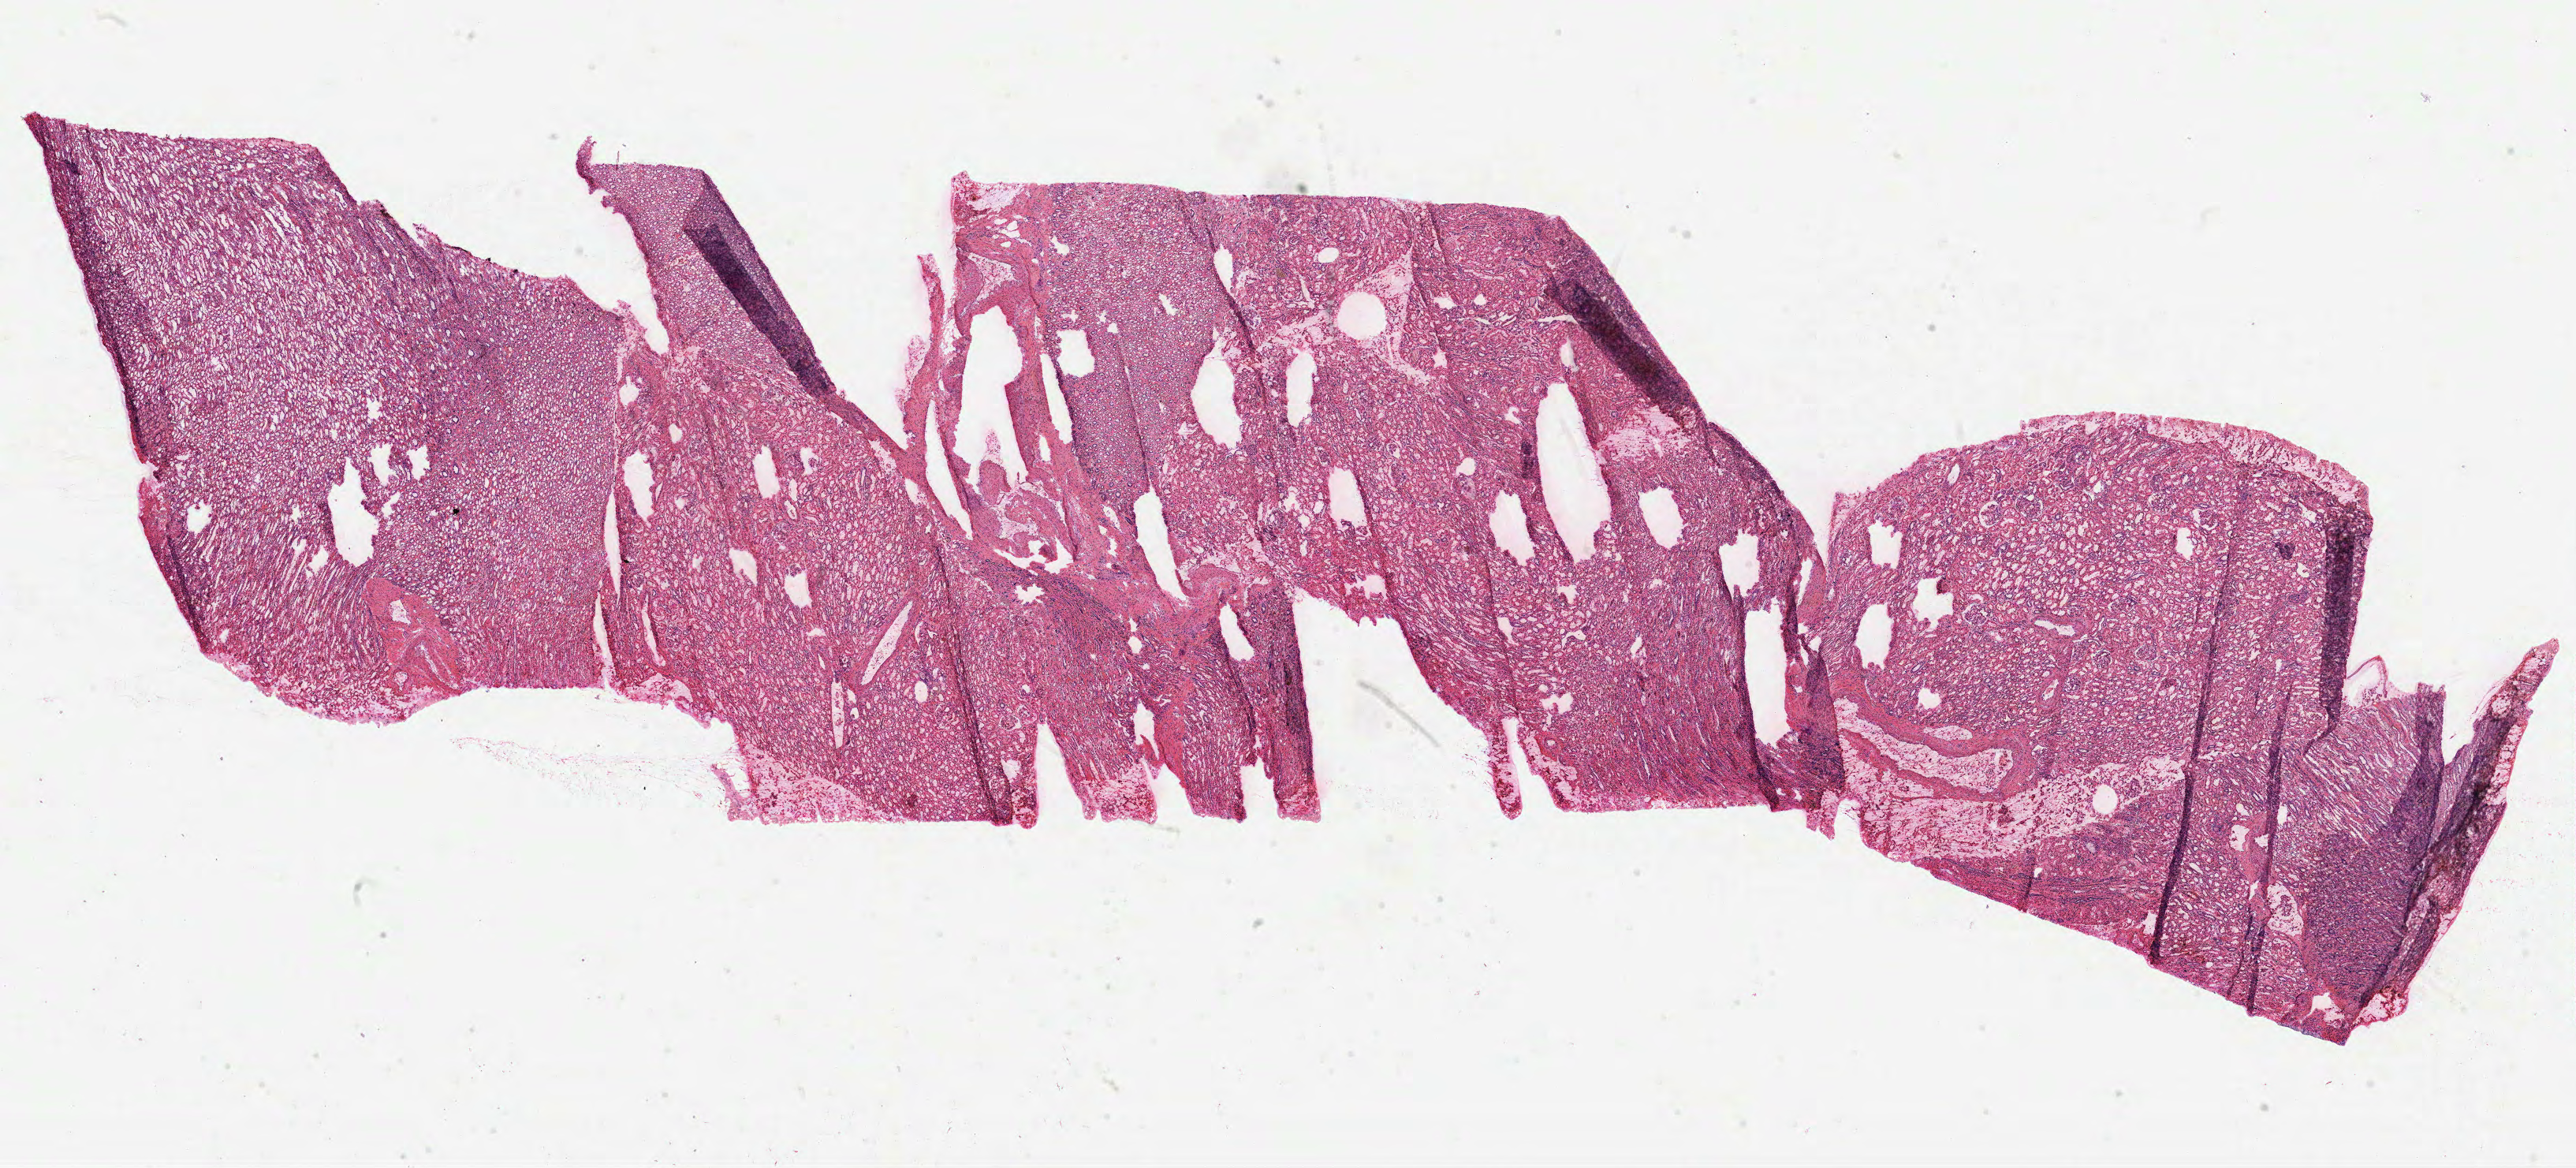
Digitized Hematoxylin and eosin (H&E) stained tissue section (whole slide) — low-resolution overview of the scanned area, about 26.3 x 11.9 mm (slide scanned at 40x), frozen section from the top of the tissue portion, sample: solid tissue normal (non-tumour tissue), kidney. Male patient; age at initial diagnosis 54 years.
• this section: solid tissue normal (non-tumour) sample from the same patient
• patient diagnosis: Clear cell adenocarcinoma, NOS